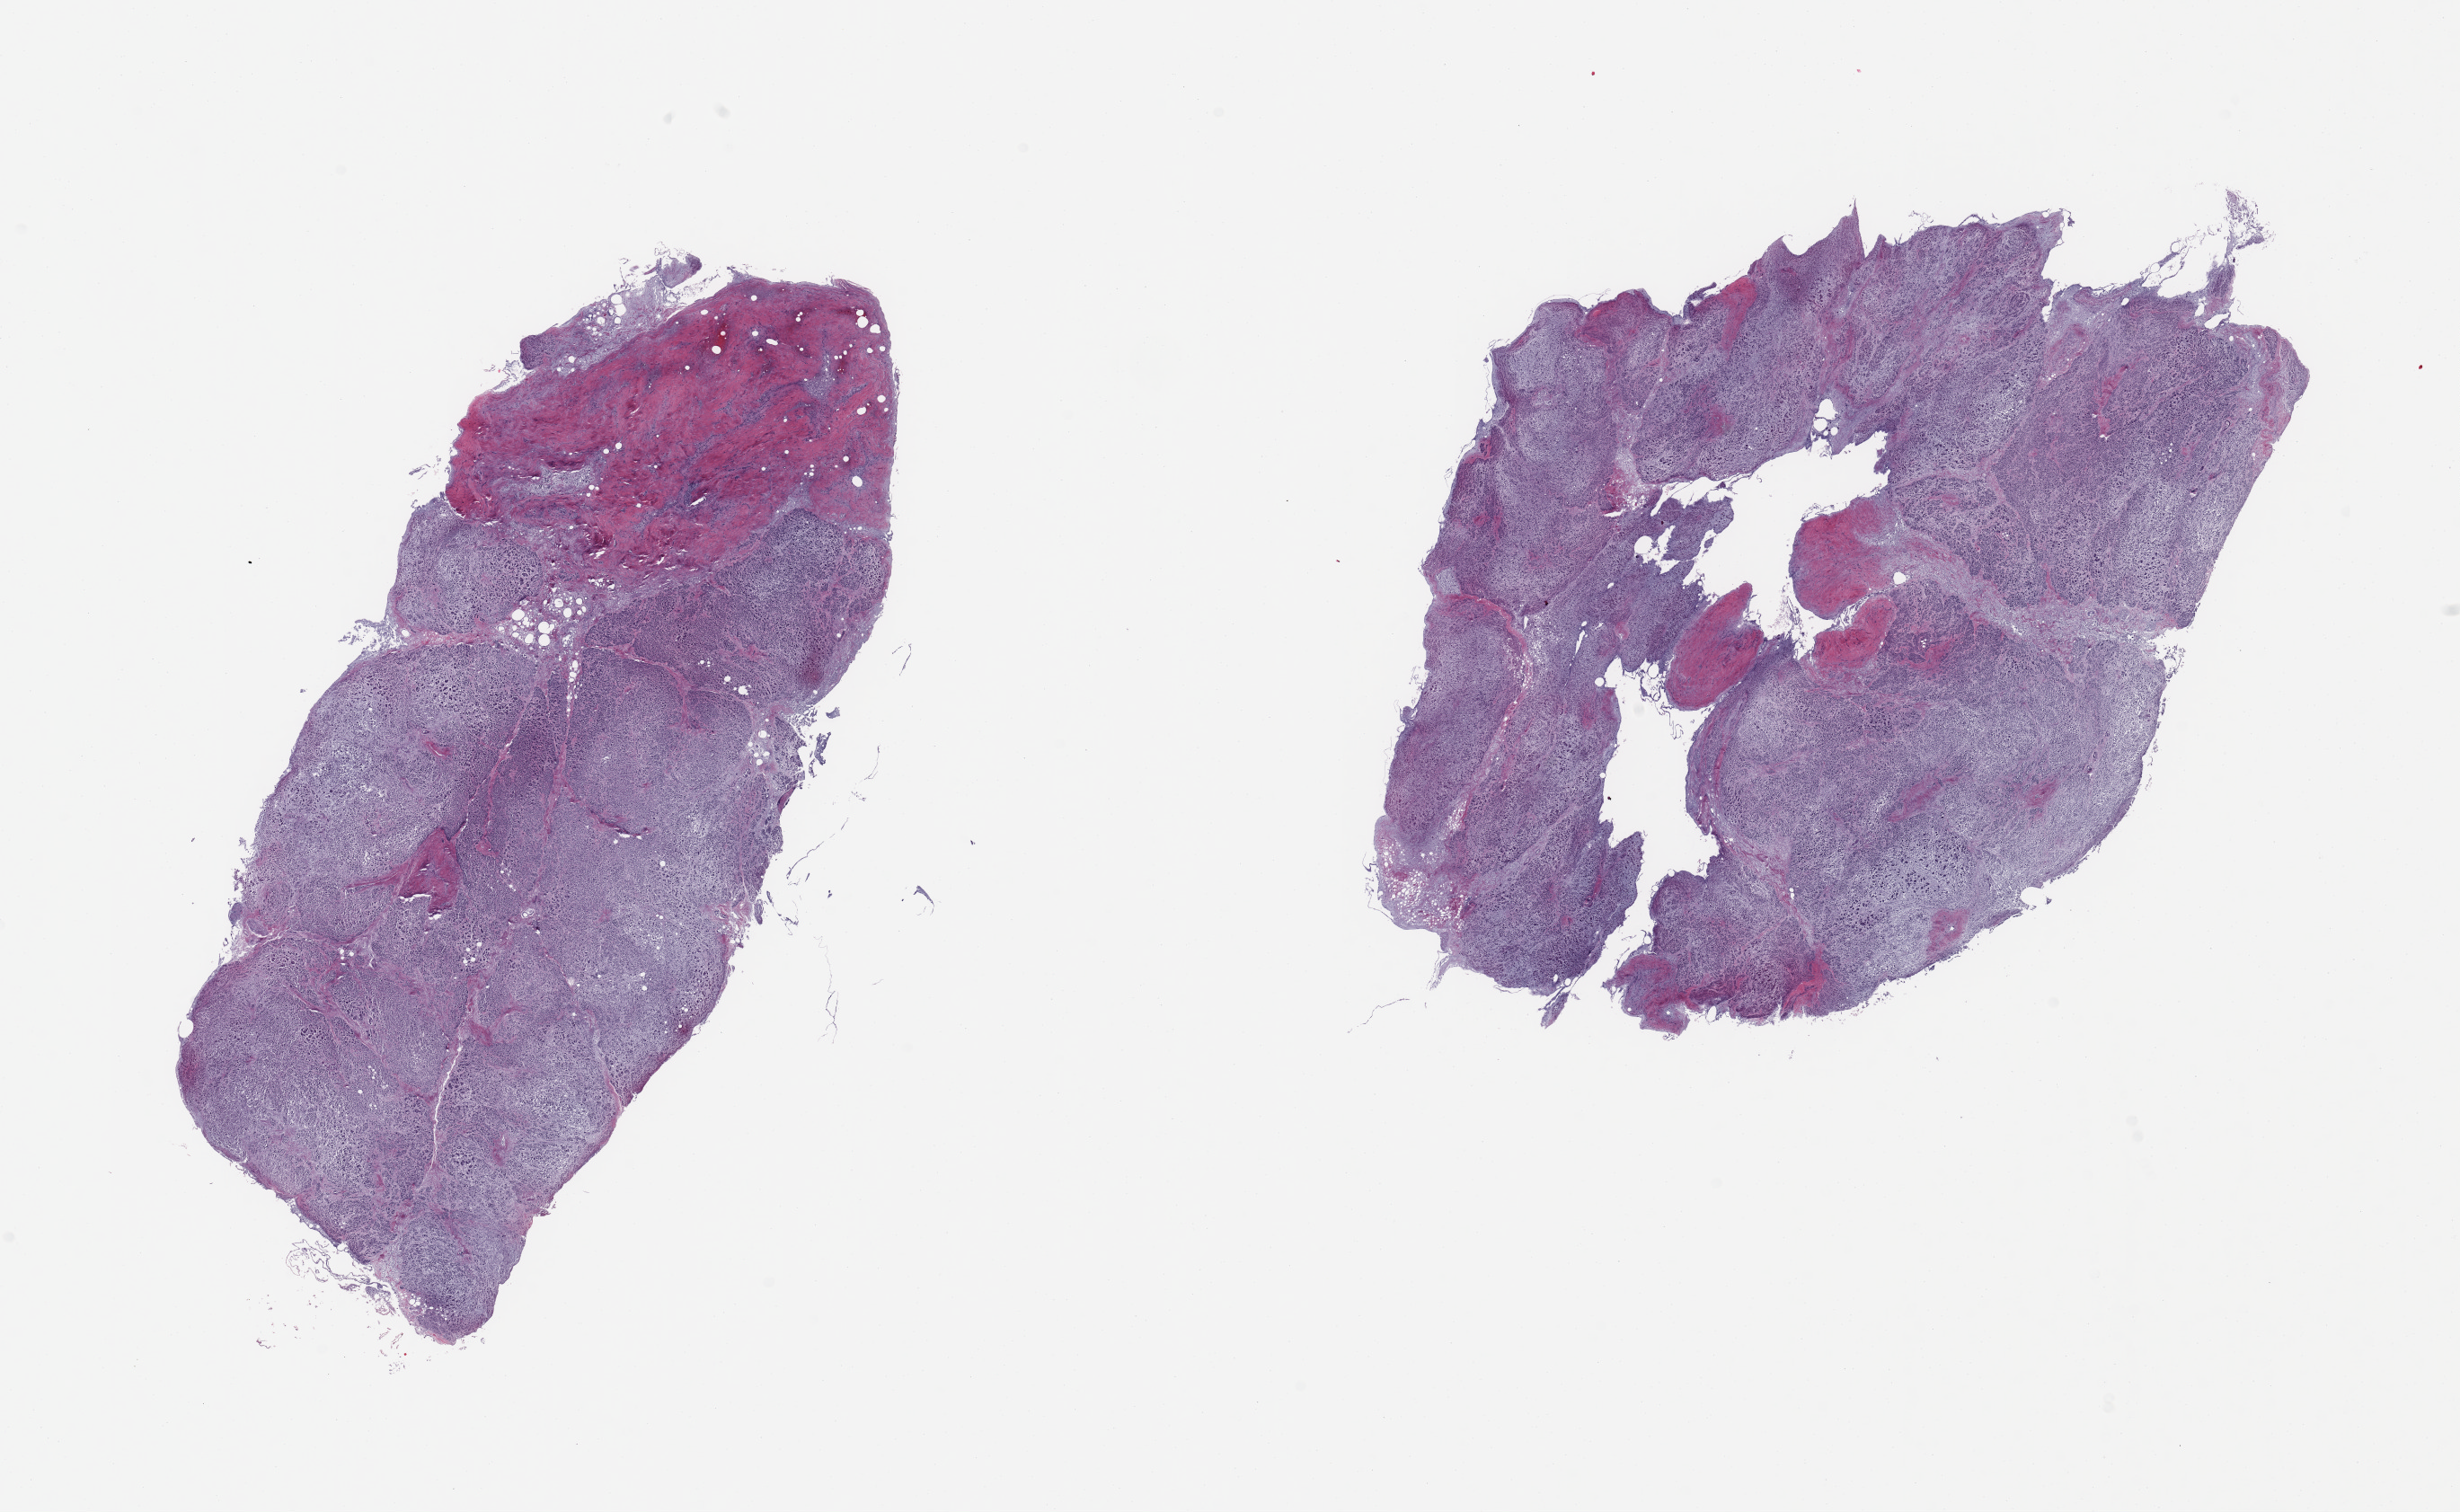
Hematoxylin and eosin (H&E) whole-slide image, a low-resolution overview of the entire scanned area, about 21.7 x 13.3 mm, PAXgene-fixed, paraffin-embedded tissue, section of pancreas (target tissue), donor tissue sample. Donor: male.
• pathologist's review note for this sample: 2 pieces, advanced saponification